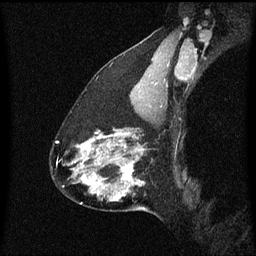
Breast MRI (dynamic contrast-enhanced), one sagittal slice; position 40 of 60 along the scan axis; dynamic contrast-enhanced series, image 2 of 3 at this slice position (ordered by acquisition); 1.5 T; TE 4.2 ms, TR 8.4 ms; 2 mm slice thickness; 256 × 256 image matrix, field of view 200 × 200 mm. Female patient, age 47 years.
Structures marked on this image (semi-automatically segmented with operator editing):
- analysis volume of interest (the breast-tissue region the enhancement analysis was run in; not a lesion): bounding box (x1, y1, x2, y2) in pixels: (81, 138, 148, 211)
- tumour enhancement mask (voxels above the 70 % enhancement threshold inside the analysis volume of interest): (81, 138, 144, 201)